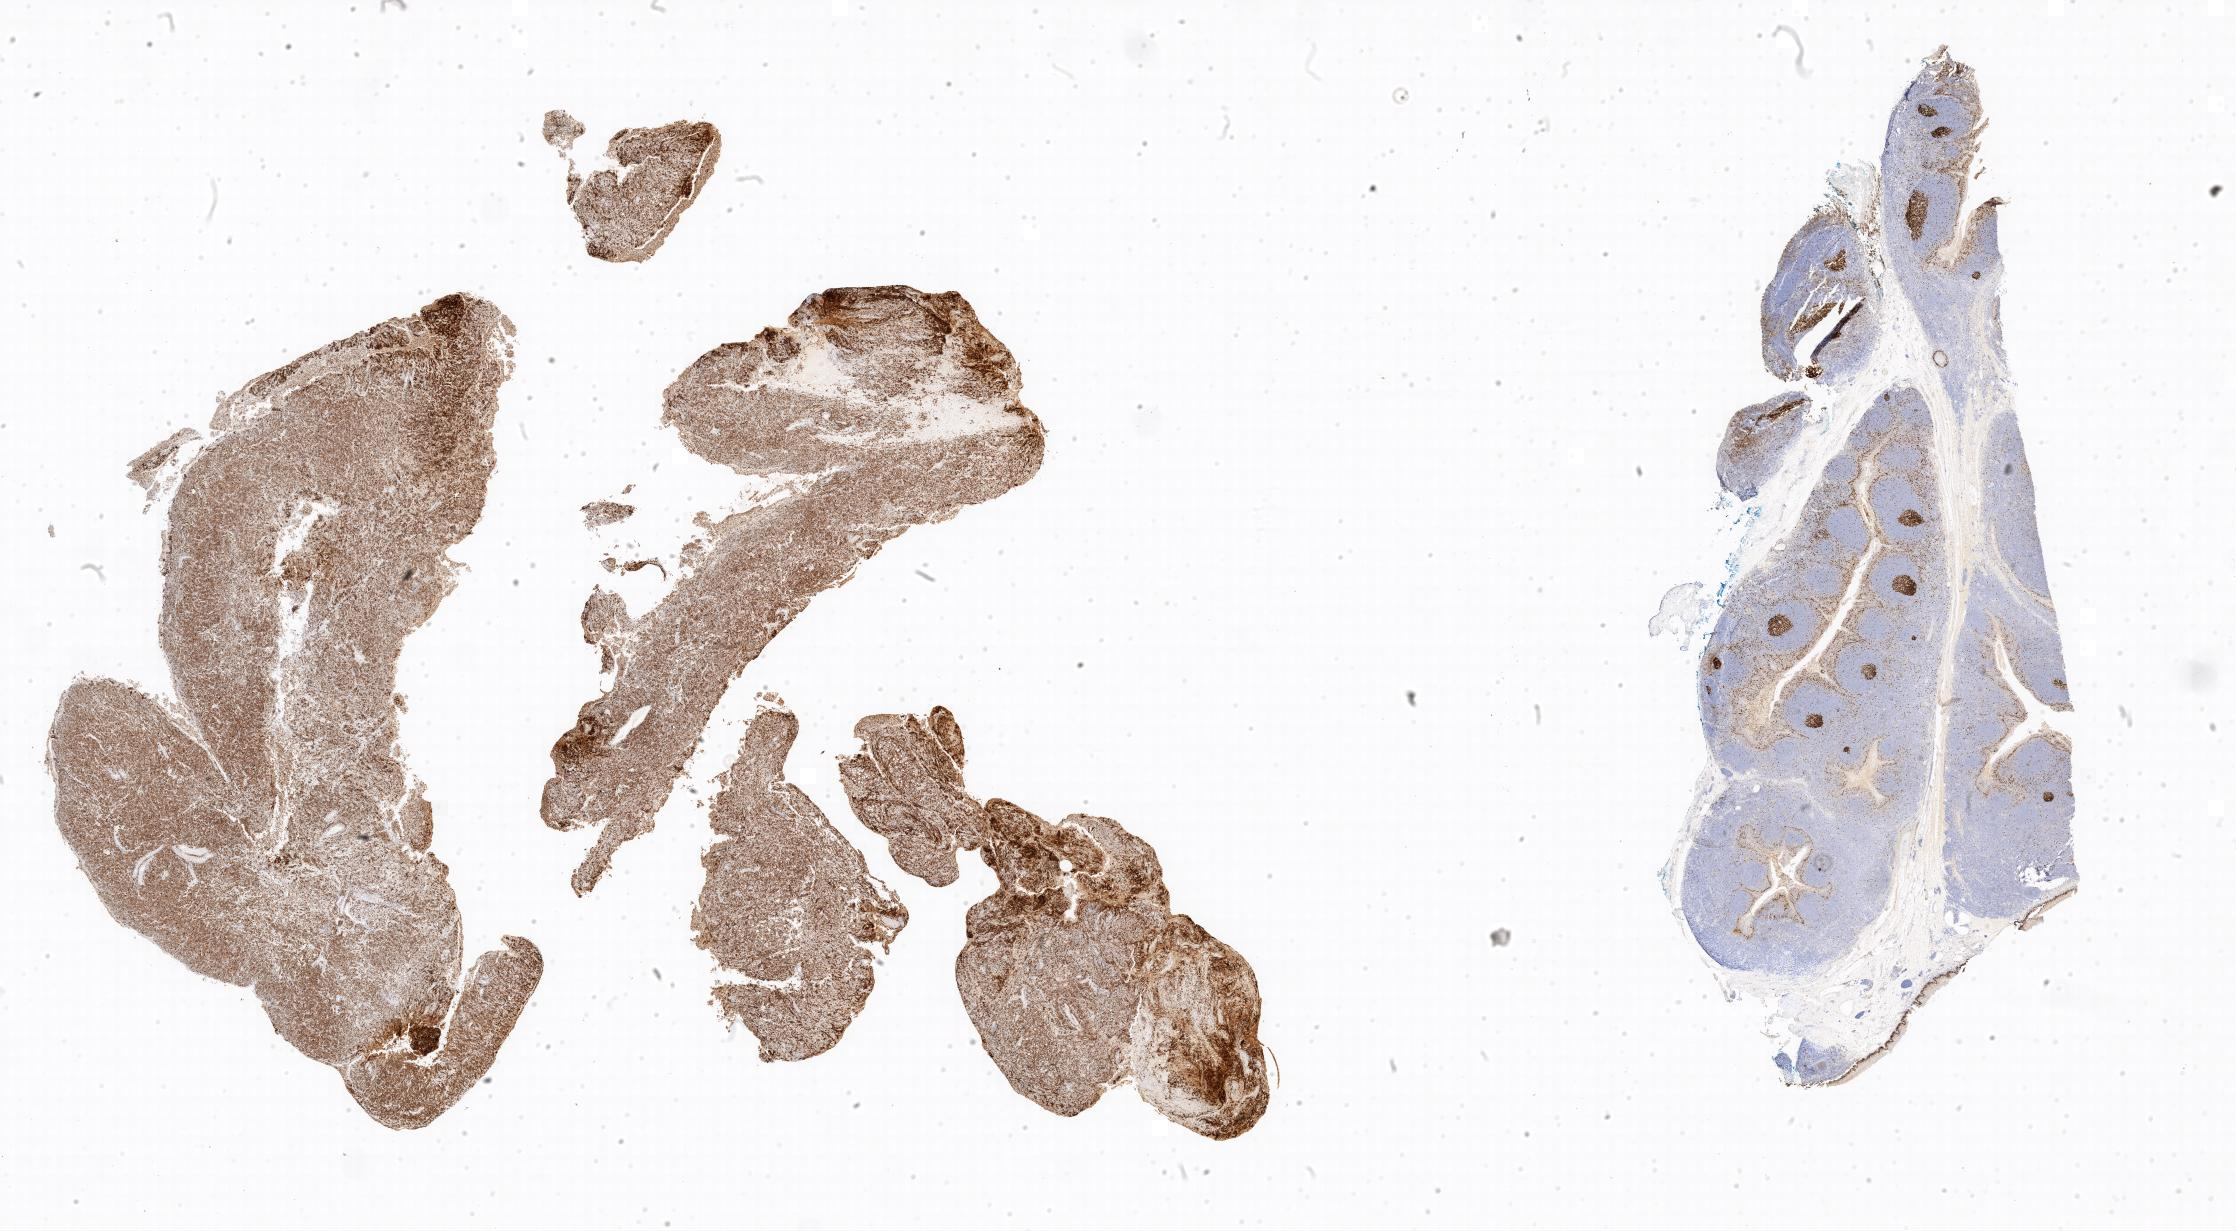
Immunohistochemistry (IHC) whole-slide image stained for Ki-67 — low-resolution overview of the scanned area, tumor tissue, anatomic site: abdomen proper. Patient: male, age at initial diagnosis 5 years.
- histologic diagnosis: Burkitt lymphoma, NOS